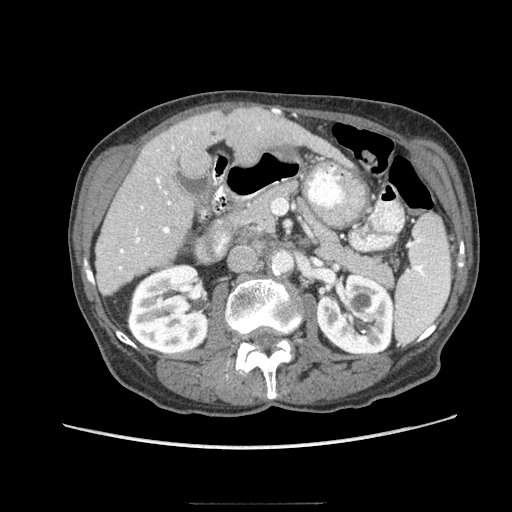
Contrast-enhanced abdominal CT (liver protocol), one axial slice. Reconstruction kernel STANDARD. 140 kVp. Soft-tissue window (W 400 / L 40 HU). 512 × 512 image matrix, field of view 360 × 360 mm. Case-level facts recorded for this patient, not image findings: diagnosis: hepatocellular carcinoma (patient treated with transarterial chemoembolisation; whether this scan precedes or follows treatment is not stated here); TNM stage (as recorded): Stage-I; Child-Pugh class: A; tumour nodularity: uninodular.
Outlined on this slice (semi-automatic segmentation, software-assisted and operator-edited):
- liver parenchyma outside the tumour (the mass and vessels are separate outlines, so this box may not span the whole liver): bounding box [x1, y1, x2, y2] px = [96, 108, 322, 294]
- liver vessels: [119, 127, 260, 270]